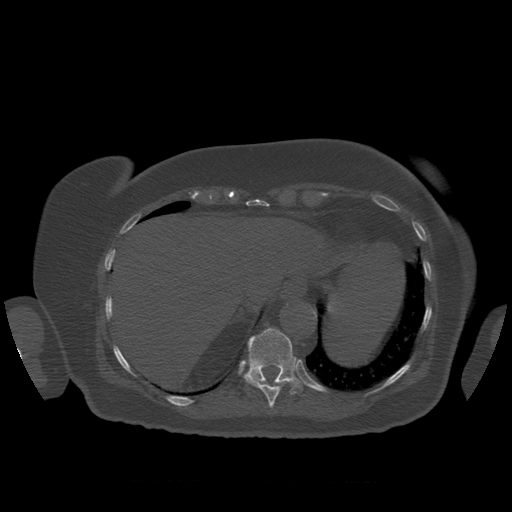
CT including the spine, one axial slice; position 330 of 399 along the scan axis; 120 kVp; bone window (W 1800 / L 400 HU); 1.25 mm slice thickness; 512 × 512 image matrix, field of view 404 × 404 mm. Patient age 81 years. Case-level facts recorded for this patient, not image findings: primary cancer: renal; vertebrae with lytic lesions (as recorded): L1.
Structures marked on this image (semi-automatic segmentation, software-assisted and operator-edited):
- T10 vertebra: bounding box (x1, y1, x2, y2) in pixels: (244, 376, 294, 409)
- T11 vertebra: (244, 328, 303, 395)